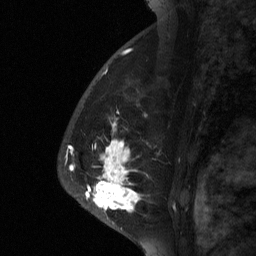
Breast MRI (dynamic contrast-enhanced), one sagittal slice. Position 44 of 64 along the scan axis. Dynamic contrast-enhanced study with each time point stored as its own series, time point 2 of 3 at this slice position (early post-contrast, ordered by acquisition time). 1.5 T. TE 4.8 ms, TR 27 ms. 2 mm slice thickness. 256 × 256 image matrix. Patient: female, 56 years. Case-level facts recorded for this patient, not image findings: setting: breast cancer imaged before/during neoadjuvant chemotherapy; receptor status: HER2-positive.
Outlined on this slice (semi-automatically segmented with operator editing):
- analysis volume of interest (the breast-tissue region the enhancement analysis was run in; not a lesion): bounding box [x1, y1, x2, y2] px = [79, 104, 182, 229]
- tumour enhancement mask (voxels above the 90 % enhancement threshold inside the analysis volume of interest): [85, 124, 140, 212]